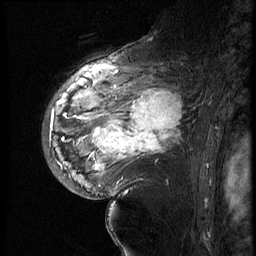
Breast MRI (dynamic contrast-enhanced), one sagittal slice. 4 images stored at this slice position (order not interpretable as contrast timing). 1.5 T. TE 4.2 ms, TR 9 ms. 2.5 mm slice thickness. 256 × 256 image matrix, field of view 180 × 180 mm. Patient: female, 56 years. Case-level facts recorded for this patient, not image findings: setting: breast cancer imaged before/during neoadjuvant chemotherapy; receptor status: HER2-positive.
Annotated regions visible in this slice (semi-automatically segmented with operator editing):
- analysis volume of interest (the breast-tissue region the enhancement analysis was run in; not a lesion): bounding box [x1, y1, x2, y2] px = [82, 83, 199, 177]
- tumour enhancement mask (voxels above the 140 % enhancement threshold inside the analysis volume of interest): [92, 91, 183, 171]